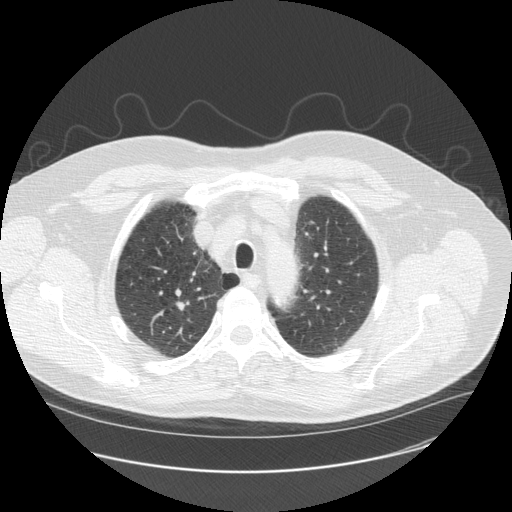
Low-dose screening chest CT, axial slice, second screening round (one year after baseline), lung window (W 1500 / L -600 HU), 2.5 mm slice thickness, slice 34 of 179 in the series, 512 × 512 image matrix. Male, age 61 years at enrolment. Former smoker at enrolment.
• Expert-annotated lung lesion, bounding box <161,289,200,326> (left, top, right, bottom; pixels).
• Screening reader's record for this exam: no non-calcified nodule ≥4 mm recorded.
• Lung cancer was diagnosed 467 days after this screen (after the third annual screen): squamous cell carcinoma, NOS, right upper lobe, moderately differentiated (G2), stage IA (AJCC 6th edition), 10 mm at pathology.